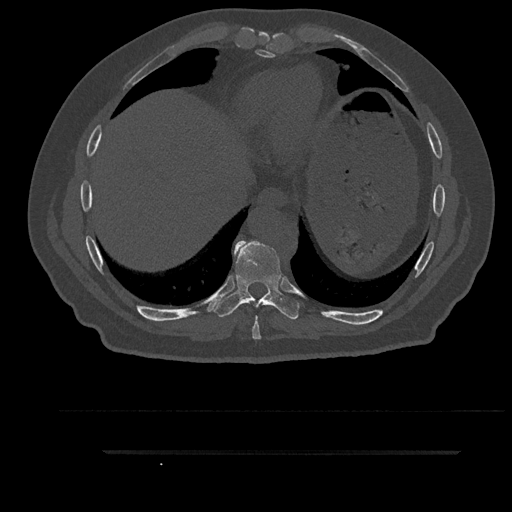
CT including the spine, one axial slice. Slice 437 of 797 in the series (ordered by position). Reconstruction kernel Br40s/3. Bone window (W 1800 / L 400 HU). 512 × 512 image matrix. Male patient, age 63 years. Case-level facts recorded for this patient, not image findings: primary cancer: renal; vertebrae with lytic lesions (as recorded): T8.
Outlined on this slice (semi-automatic segmentation, software-assisted and operator-edited):
- T8 vertebra: bounding box <252,305,273,340> (left, top, right, bottom; pixels)
- T9 vertebra: <212,241,300,320>